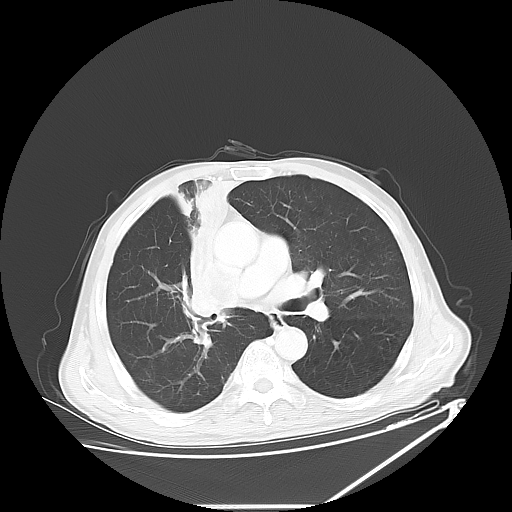
Chest CT, one axial slice; slice 36 of 60 in the series (ordered by position); reconstruction kernel LUNG; 120 kVp; lung window (W 1500 / L -600 HU); 5 mm slice thickness; 512 × 512 image matrix, field of view 410 × 410 mm. Male patient, age 73 years. Case-level facts recorded for this patient, not image findings: clinical TNM (as recorded): T2a N1 M0.
Annotated regions visible in this slice (rectangle marked by the reading radiologist):
- lung tumour (recorded histology: squamous cell carcinoma): box from (x=174, y=172) to (x=228, y=333) px